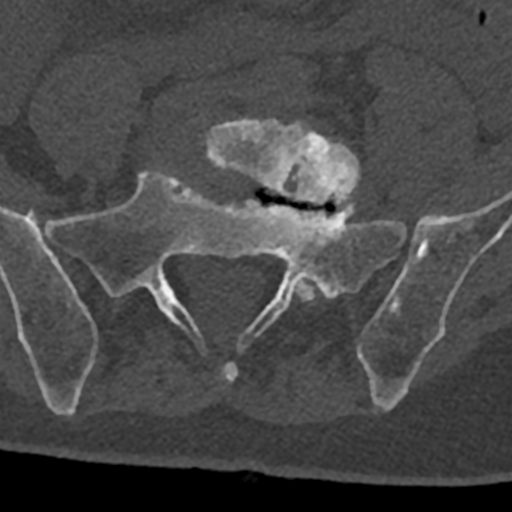
CT including the spine, one axial slice. Position 161 of 797 along the scan axis. Reconstruction kernel Br40s/3. 120 kVp. Bone window (W 1800 / L 400 HU). 512 × 512 image matrix, field of view 160 × 160 mm. Male patient, age 74 years. From the clinical record (not read from this slice): primary cancer: renal.
Outlined on this slice (semi-automatic segmentation, software-assisted and operator-edited):
- L5 vertebra: bounding box <205,118,360,302> (left, top, right, bottom; pixels)